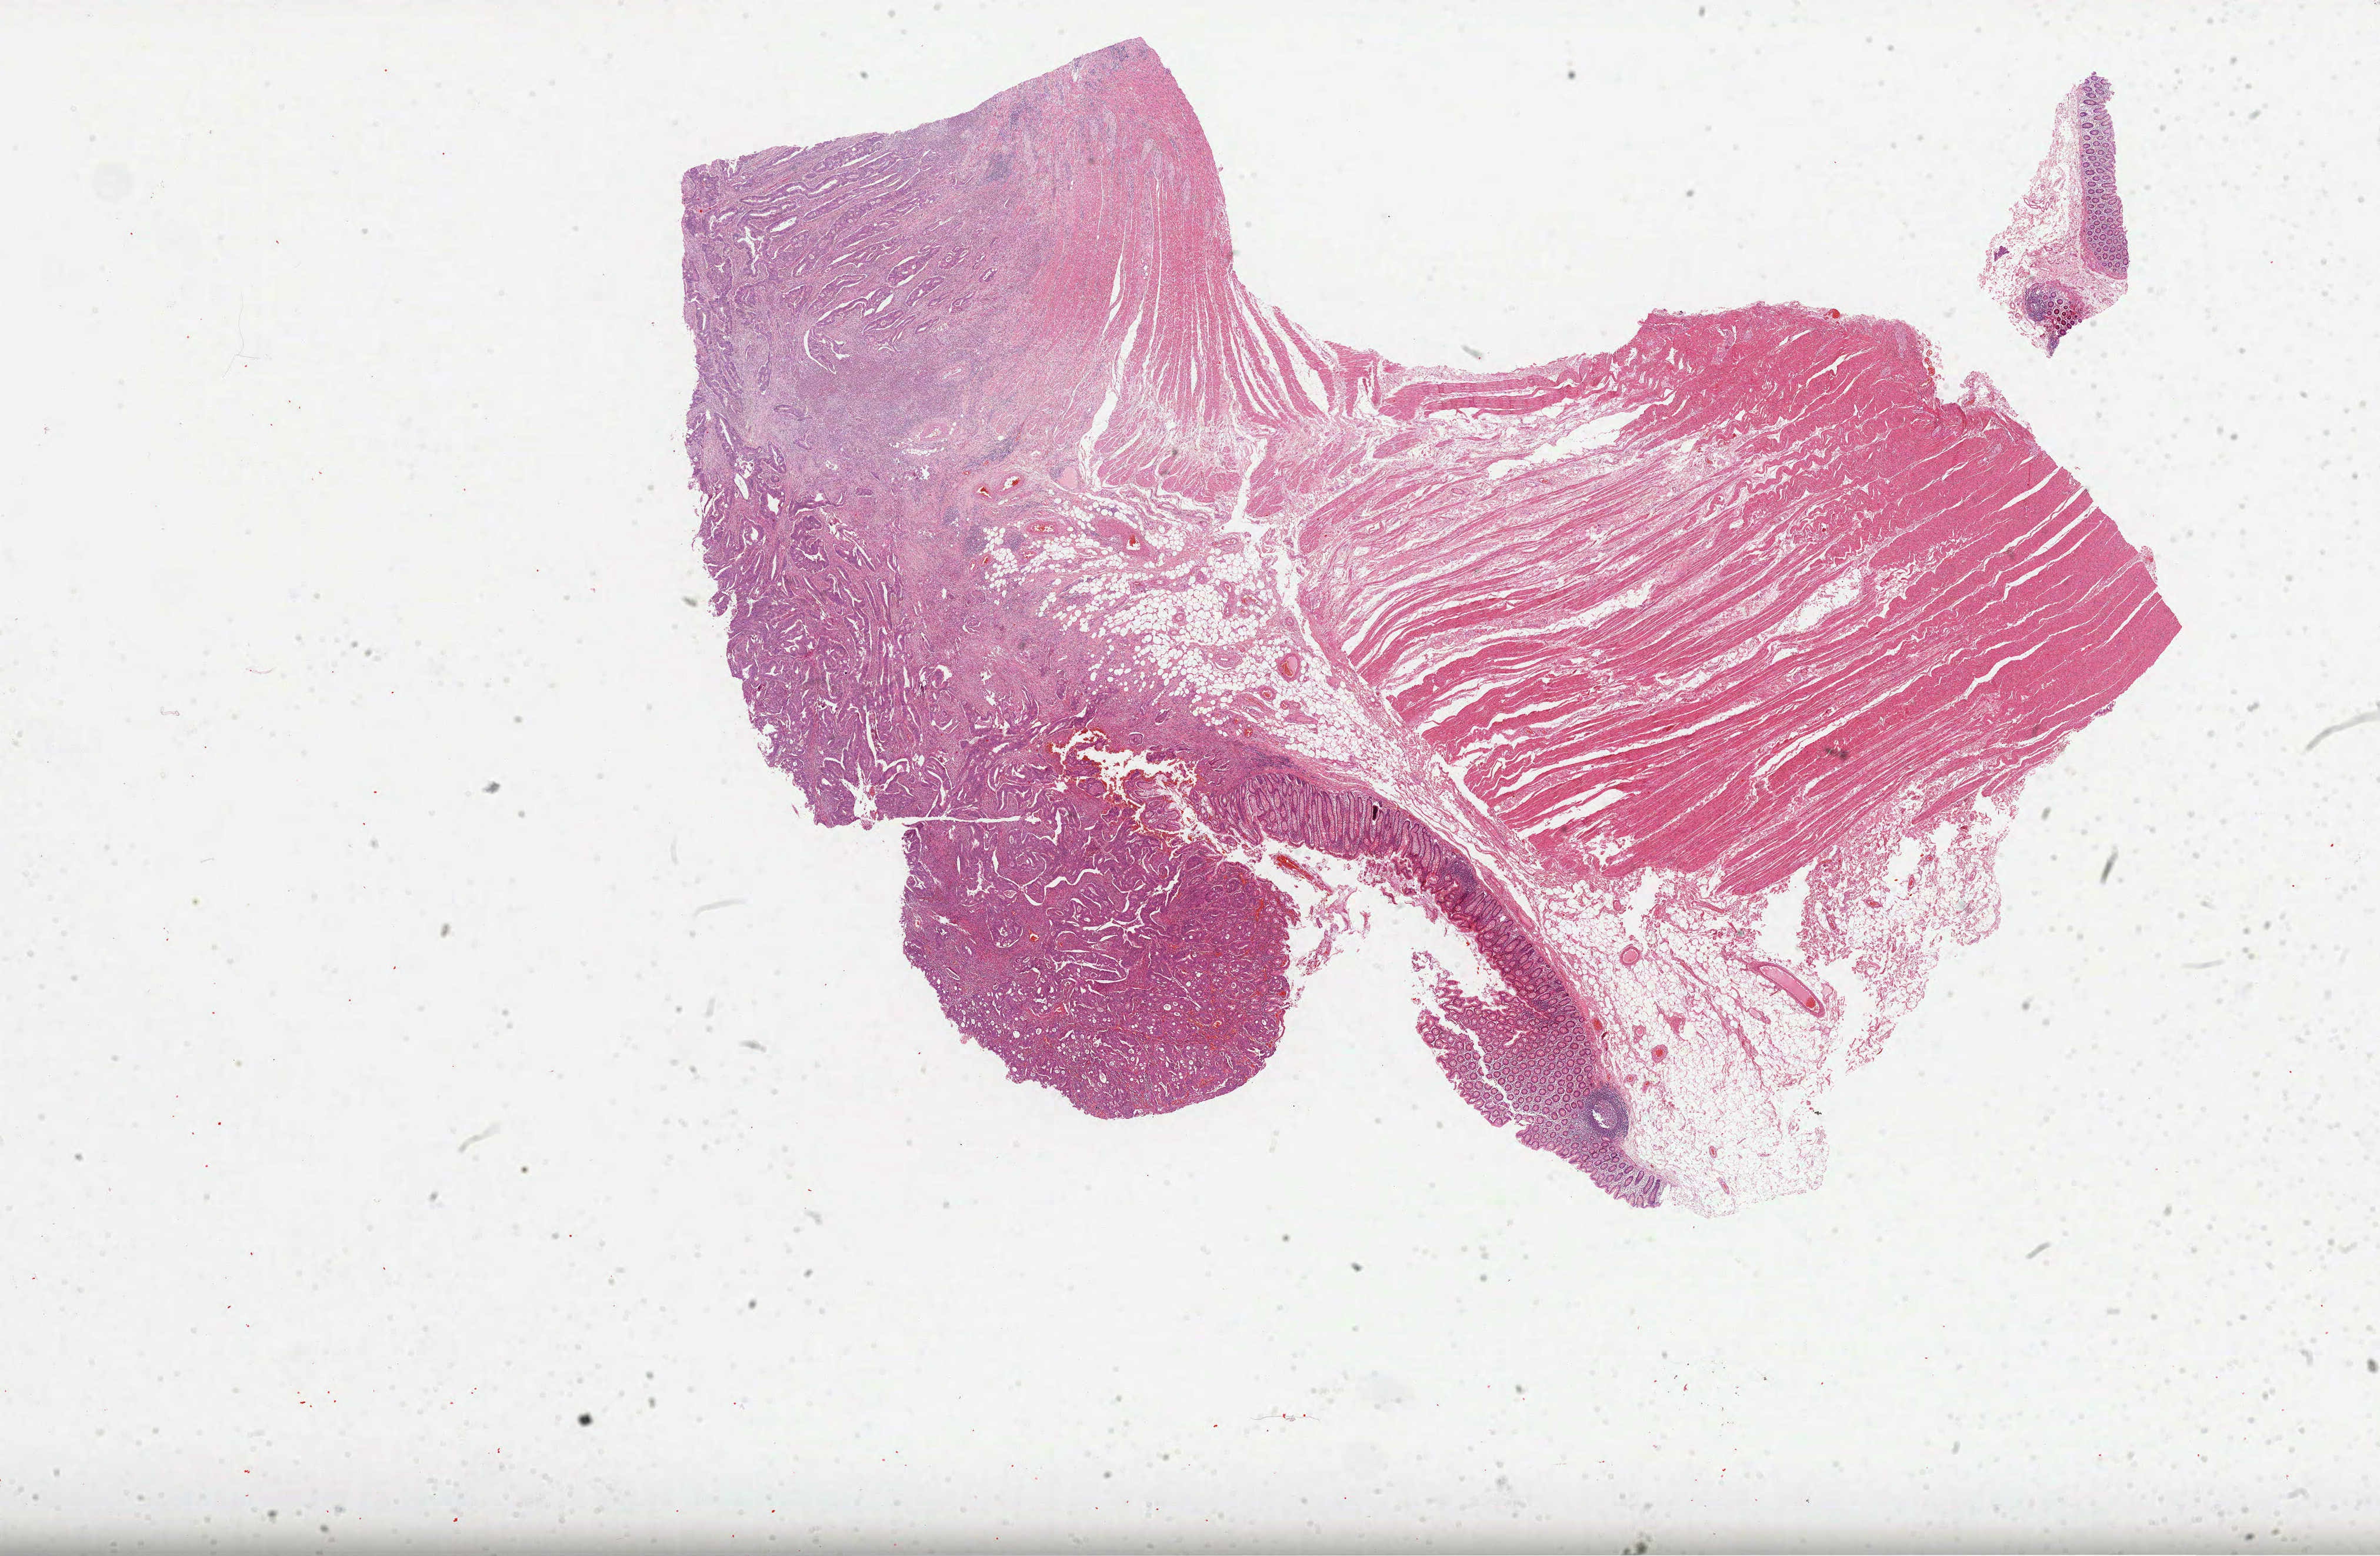
Whole-slide histology image, Hematoxylin and eosin (H&E) stained, whole scanned area (about 32.6 x 21.3 mm) shown as a low-resolution overview, formalin-fixed paraffin-embedded (FFPE) diagnostic section, sample: primary tumour, colon. Male, age 69 years at initial diagnosis.
Histologic diagnosis: Adenocarcinoma, NOS.